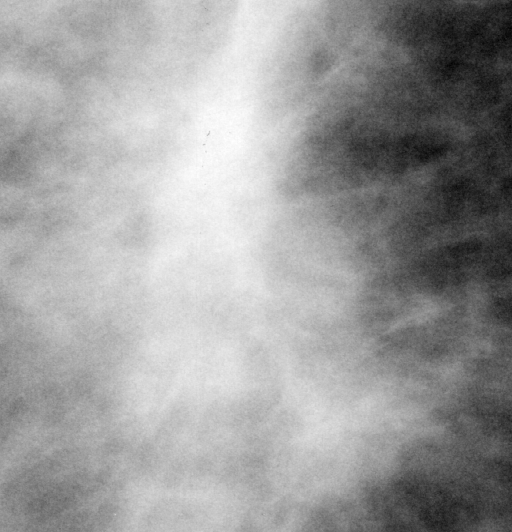
Crop from a digitized film mammogram around one marked abnormality, right breast, CC view, BI-RADS breast density category 3 (scale 1–4).
Mass, shape architectural distortion, margins spiculated; BI-RADS assessment category 5; pathology (as recorded): malignant.